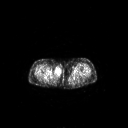
FDG PET of an extremity soft-tissue mass (from a PET/CT study), one axial slice; position 230 of 311 along the scan axis; 3.27 mm slice thickness; 128 × 128 image matrix, field of view 700 × 700 mm. Female patient, age 78 years. From the clinical record (not read from this slice): histological type: leiomyosarcoma; grade: intermediate; site of the primary tumour: parascapusular.
Structures marked on this image (expert contour drawn on MRI and transferred to this co-registered scan by the dataset authors):
- gross tumour volume including surrounding oedema: bounding box [x1, y1, x2, y2] px = [54, 67, 61, 76]
- gross tumour volume (mass): [54, 68, 61, 75]